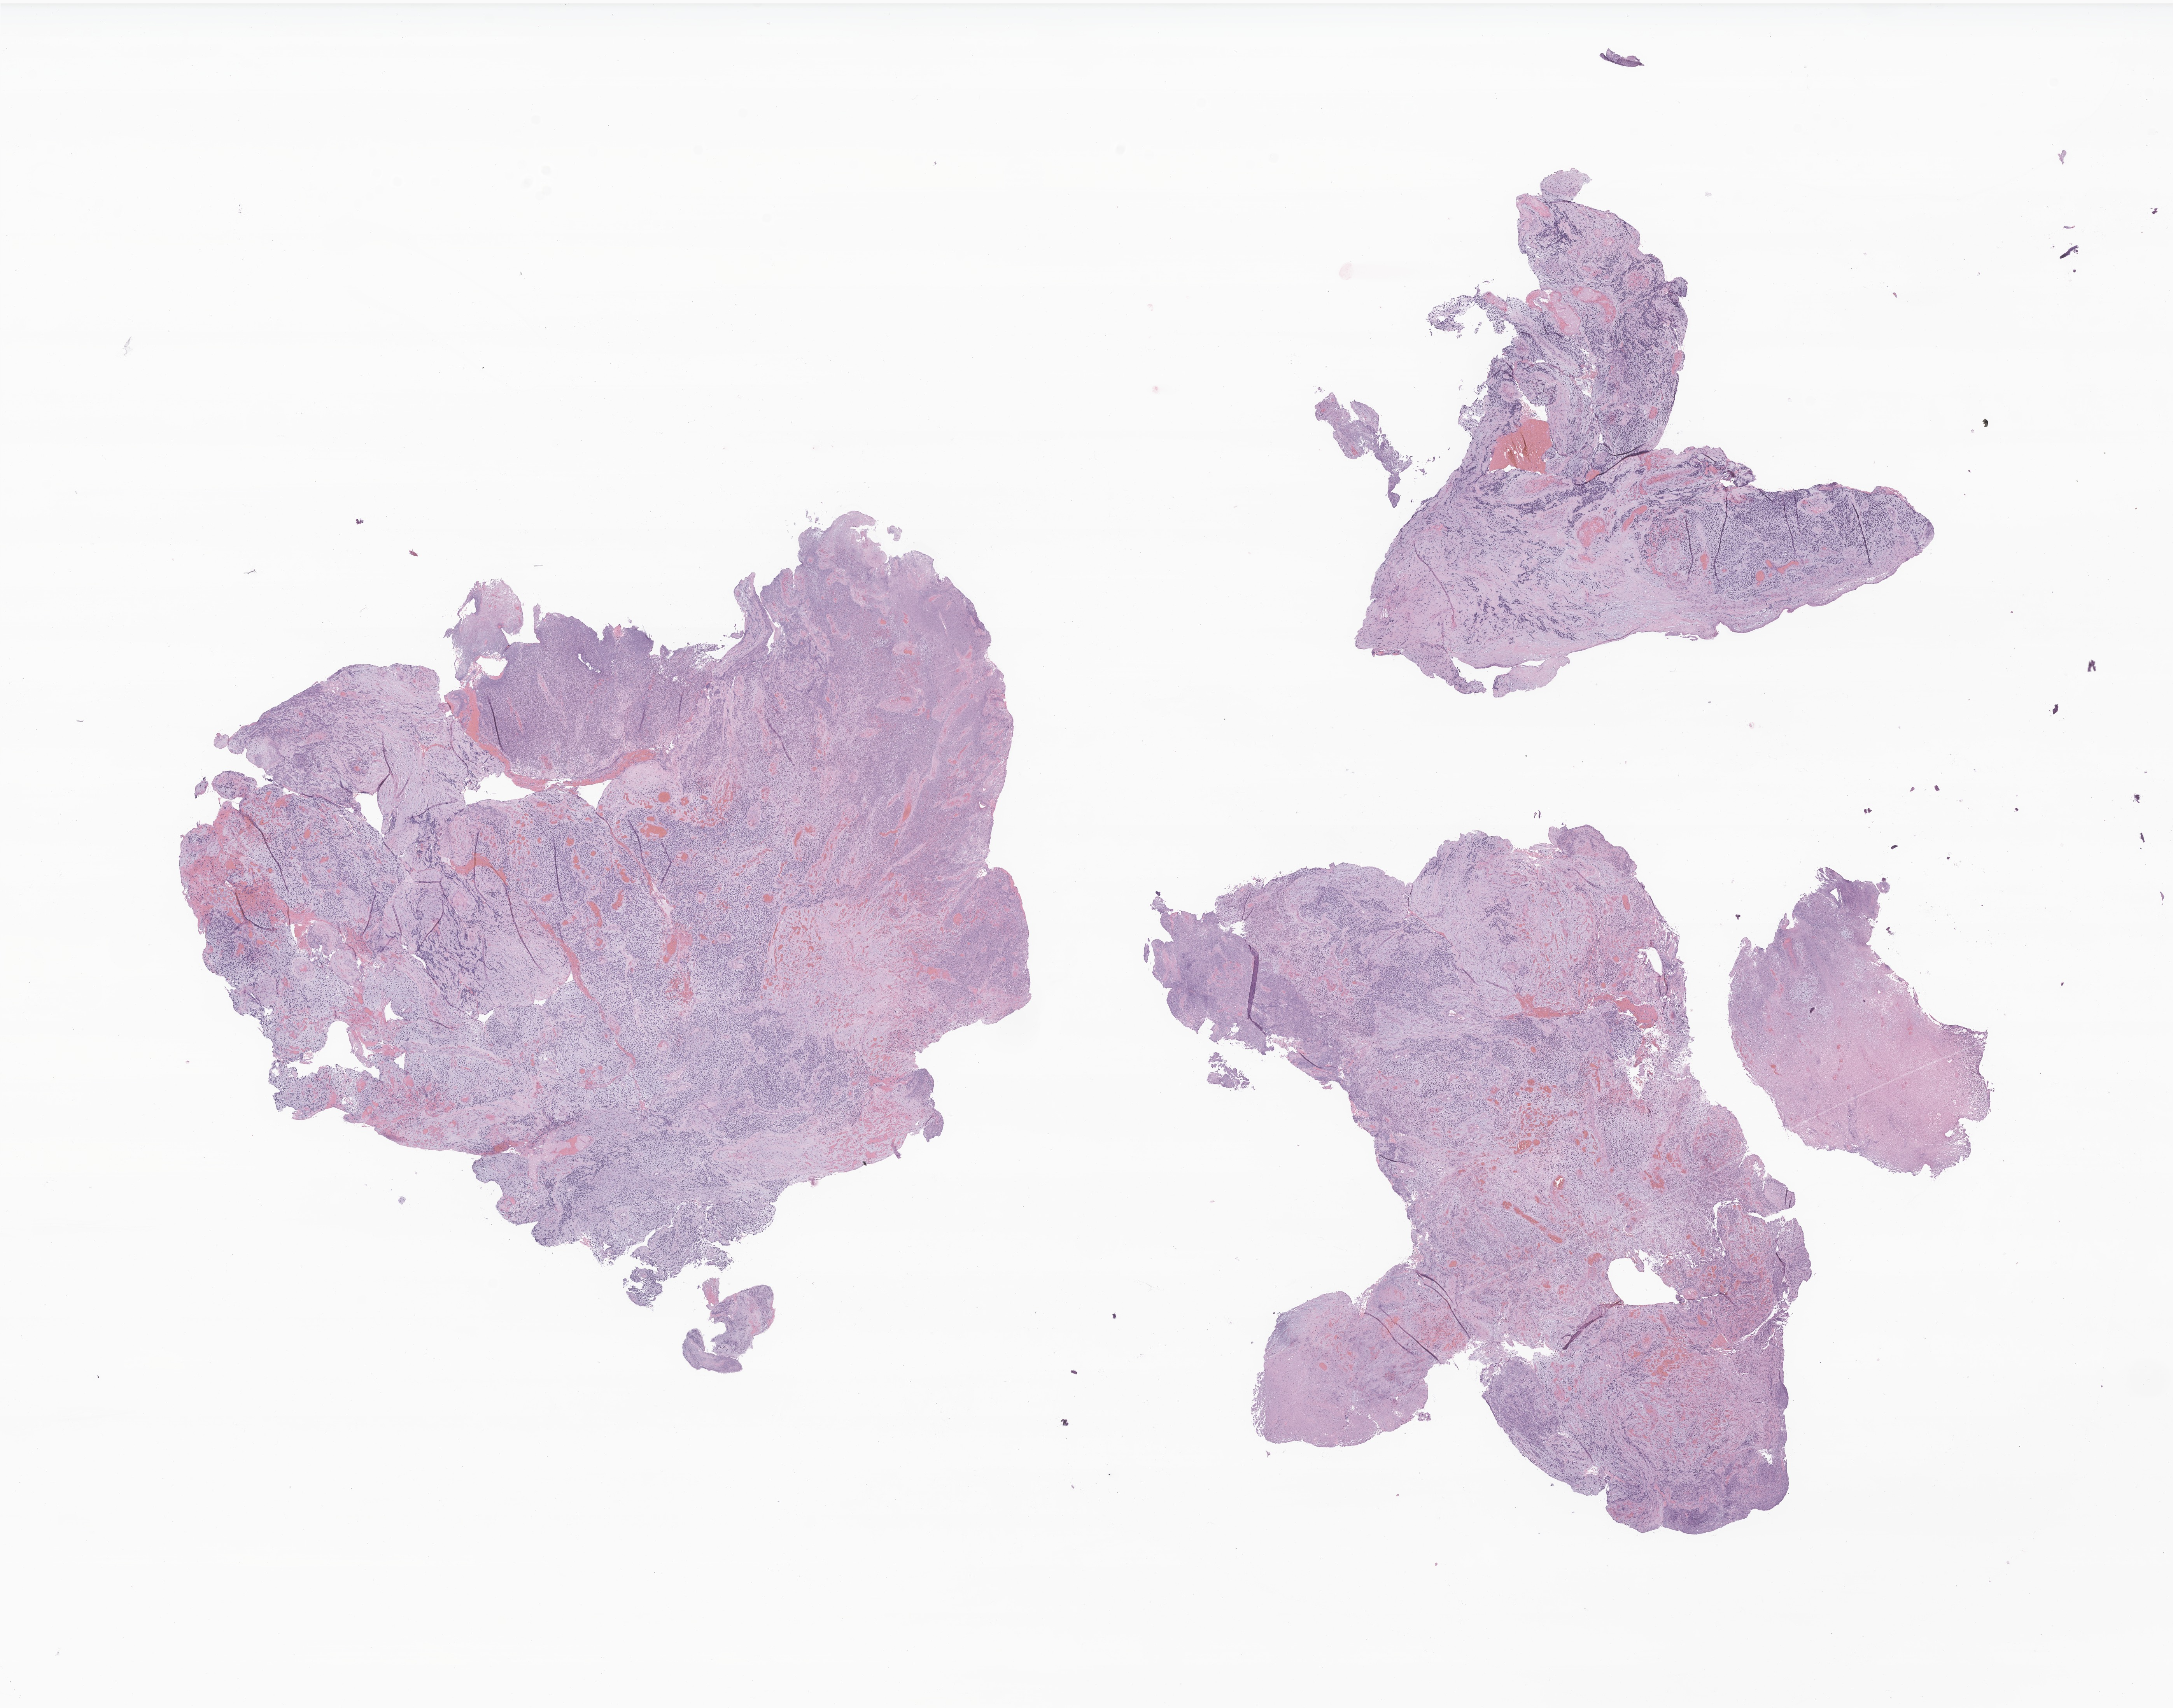
Whole-slide image, haematoxylin and eosin stain of tumor tissue from the nasopharynx, low-resolution overview of the scanned area, about 23.6 x 18.5 mm; formalin-fixed, paraffin-embedded (FFPE) tissue. Patient: female, age 149 months (12 years 5 months).
Recorded diagnosis: Embryonal rhabdomyosarcoma, NOS.